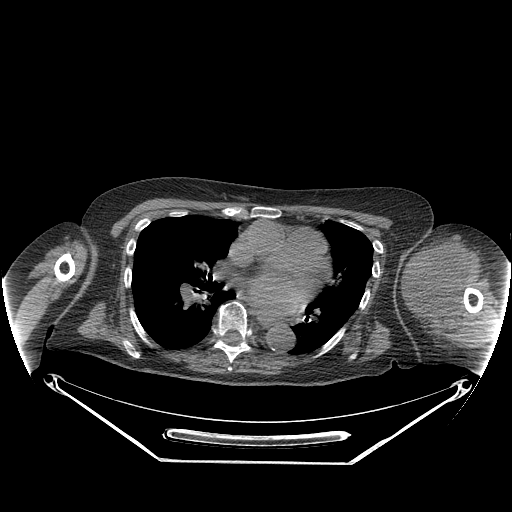
CT of an extremity soft-tissue mass (from a PET/CT study), one axial slice. Slice 174 of 267 in the series (ordered by position). Reconstruction kernel STANDARD. 140 kVp. Soft-tissue window (W 400 / L 40 HU). 3.75 mm slice thickness. 512 × 512 image matrix. Female patient. Case-level facts recorded for this patient, not image findings: histological type: pleiomorphic leiomyosarcoma; grade: high; site of the primary tumour: left biceps.
Structures marked on this image (expert contour drawn on MRI and transferred to this co-registered scan by the dataset authors):
- gross tumour volume including surrounding oedema: box from (x=404, y=233) to (x=473, y=325) px
- gross tumour volume (mass): (x=404, y=235)–(x=469, y=316)